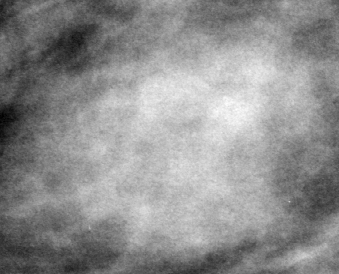
Region of interest cut from a scanned film mammogram (one marked finding), left breast, CC view, BI-RADS breast density category 3 (scale 1–4).
Mass, shape lobulated, margins circumscribed; BI-RADS assessment category 3; subtlety rating 3 on a 1 (subtle) to 5 (obvious) scale; pathology (as recorded): benign.